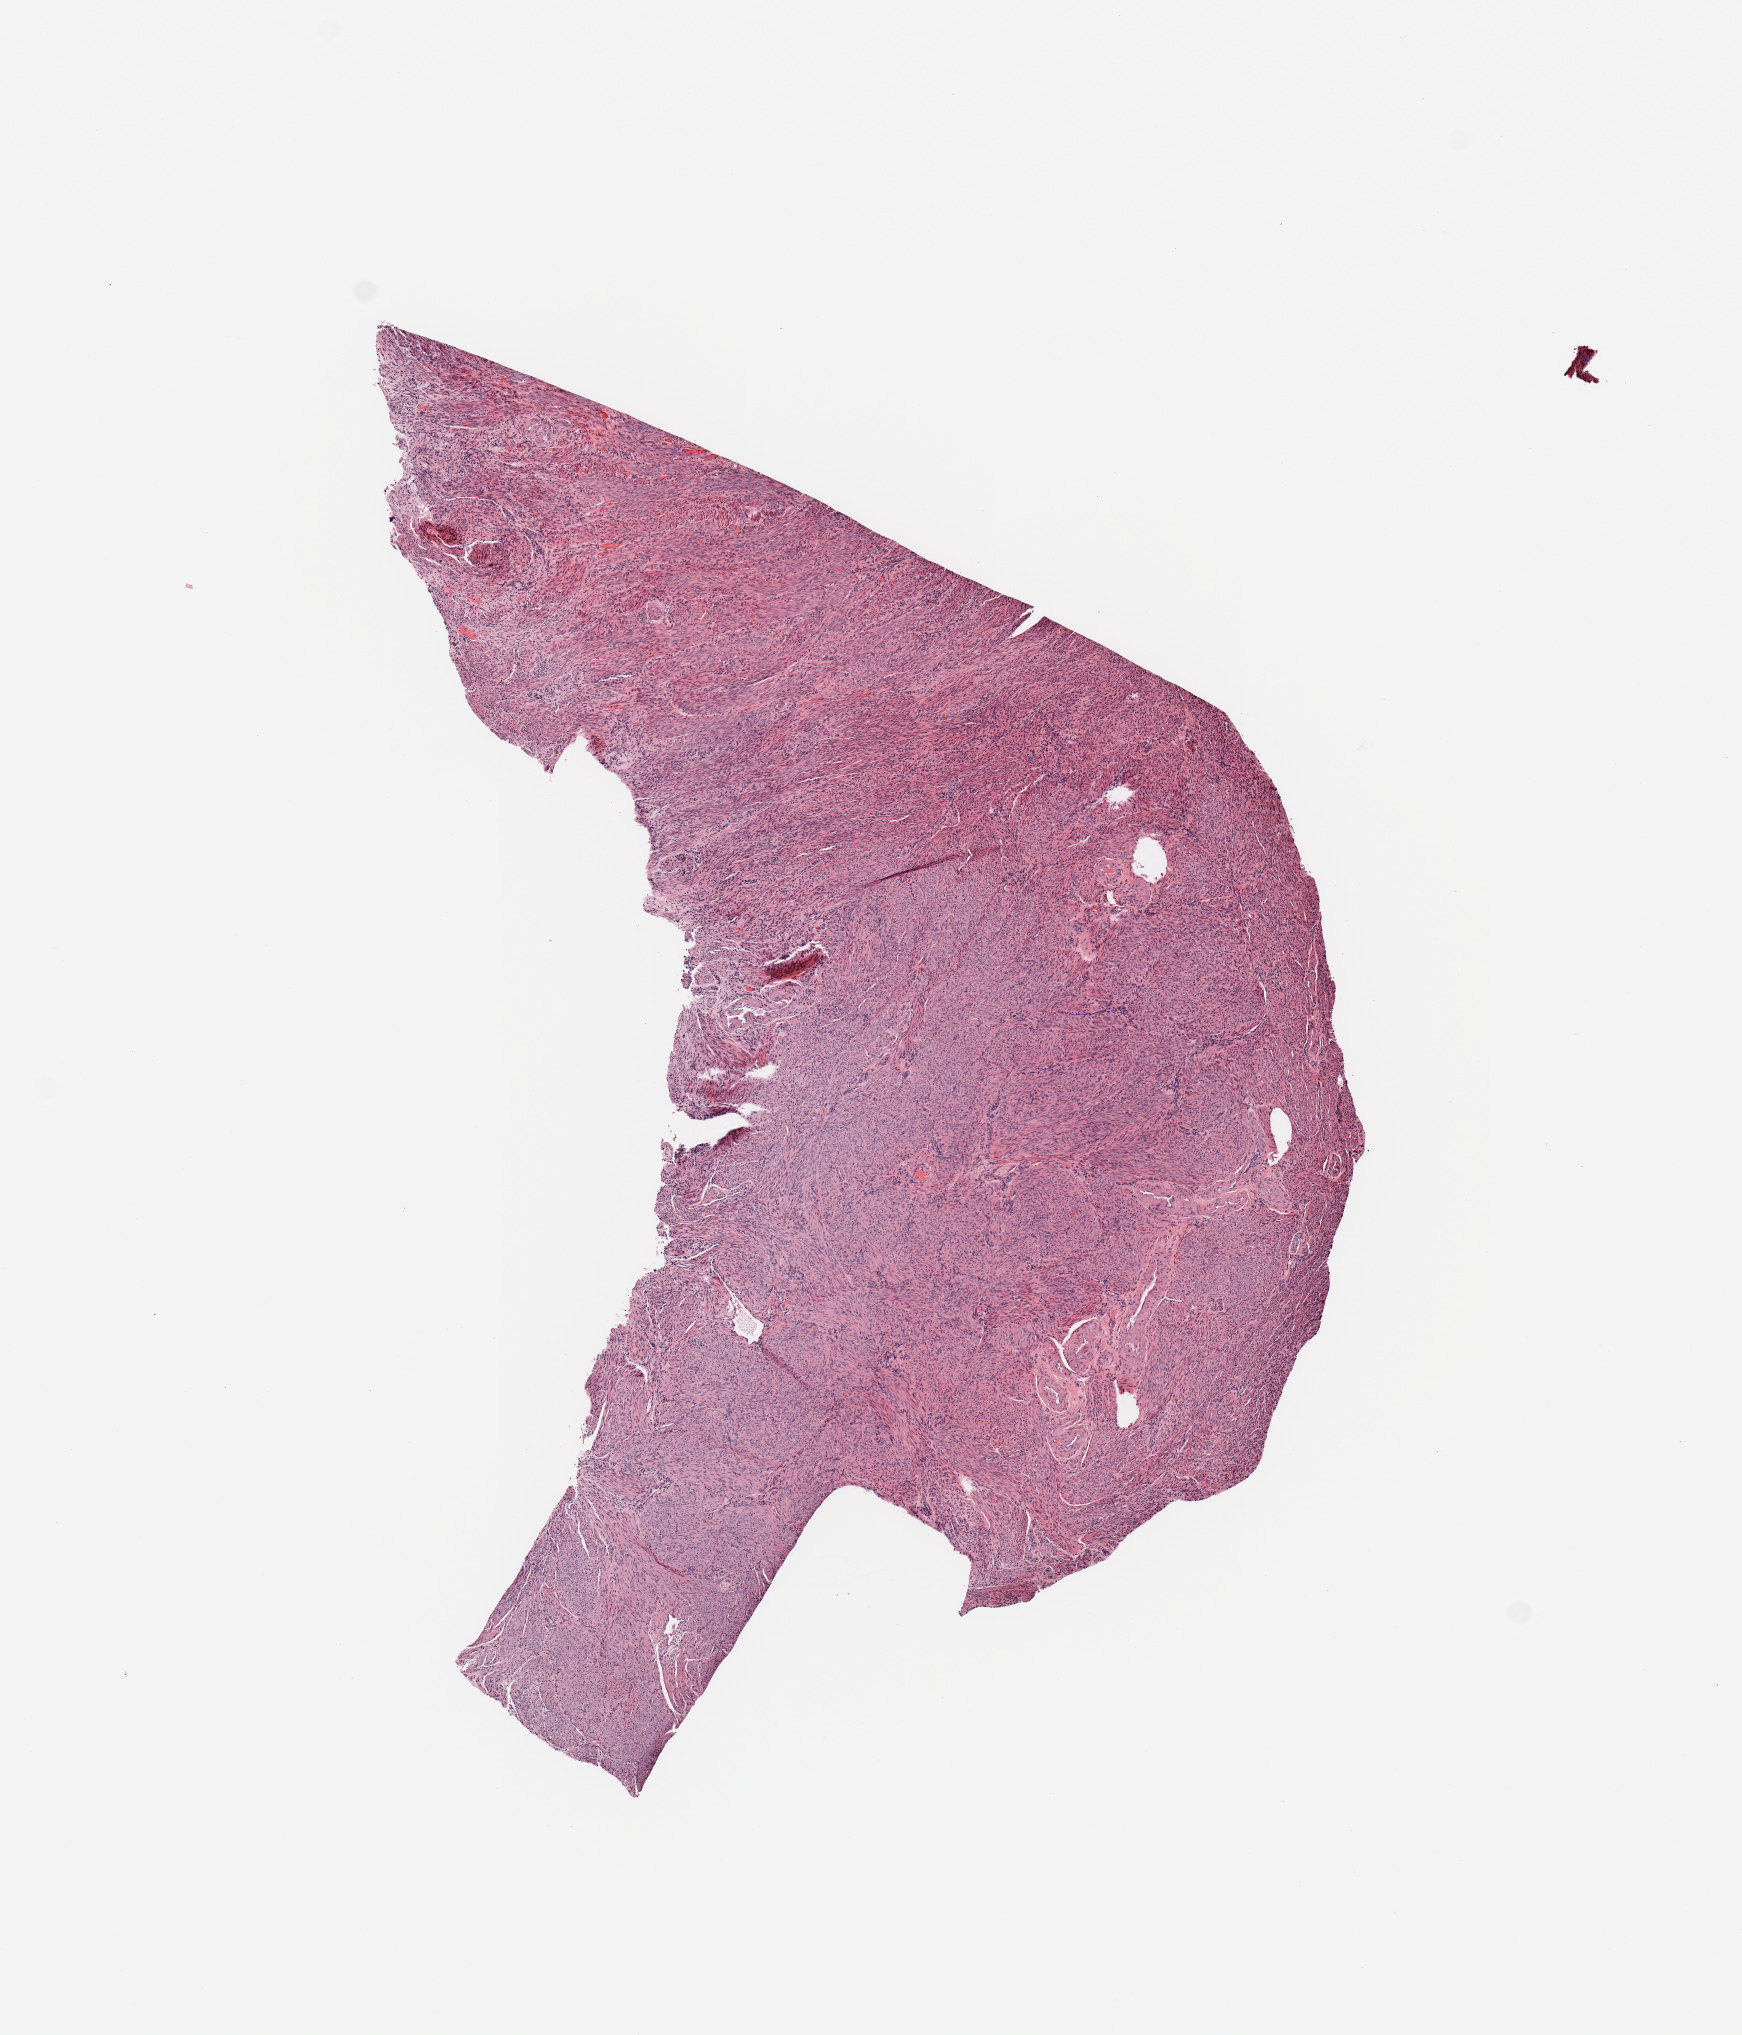
Digitized H&E tissue section (whole slide) — shown as a low-resolution overview of the whole scanned area (about 6.9 x 8.0 mm), normal (non-tumour) tissue sample, uterus. 63-year-old female patient.
• this section: normal (non-tumour) tissue from the same patient
• patient diagnosis: Endometrioid adenocarcinoma, NOS